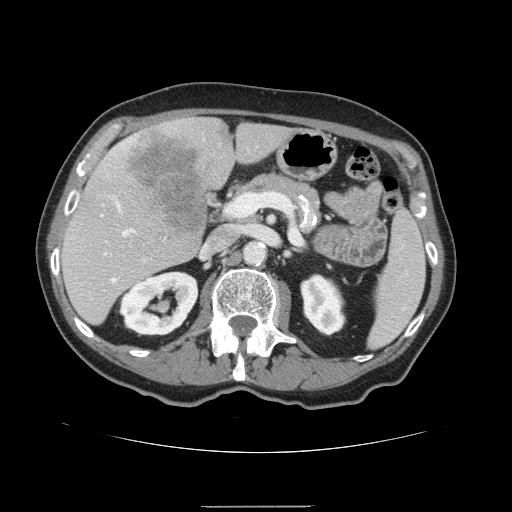
Contrast-enhanced abdominal CT, one axial slice. Slice 80 of 168 in the series (ordered by position). 120 kVp. Intravenous contrast given. Soft-tissue window (W 400 / L 40 HU). 2.5 mm slice thickness. 512 × 512 image matrix, field of view 386 × 386 mm. Male patient, age 74 years. From the clinical record (not read from this slice): diagnosis: colorectal cancer liver metastases, imaged before liver resection; multiple liver metastases: no; largest metastasis: 14.5 cm.
Annotated regions visible in this slice (outlined manually by an expert reader):
- hepatic veins: box from (x=113, y=202) to (x=135, y=281) px
- liver: (x=61, y=117)–(x=294, y=326)
- planned liver remnant (the part of the liver to remain after resection): (x=61, y=123)–(x=295, y=326)
- portal vein (with intrahepatic branches): (x=103, y=199)–(x=240, y=263)
- liver metastasis: (x=125, y=131)–(x=212, y=237)